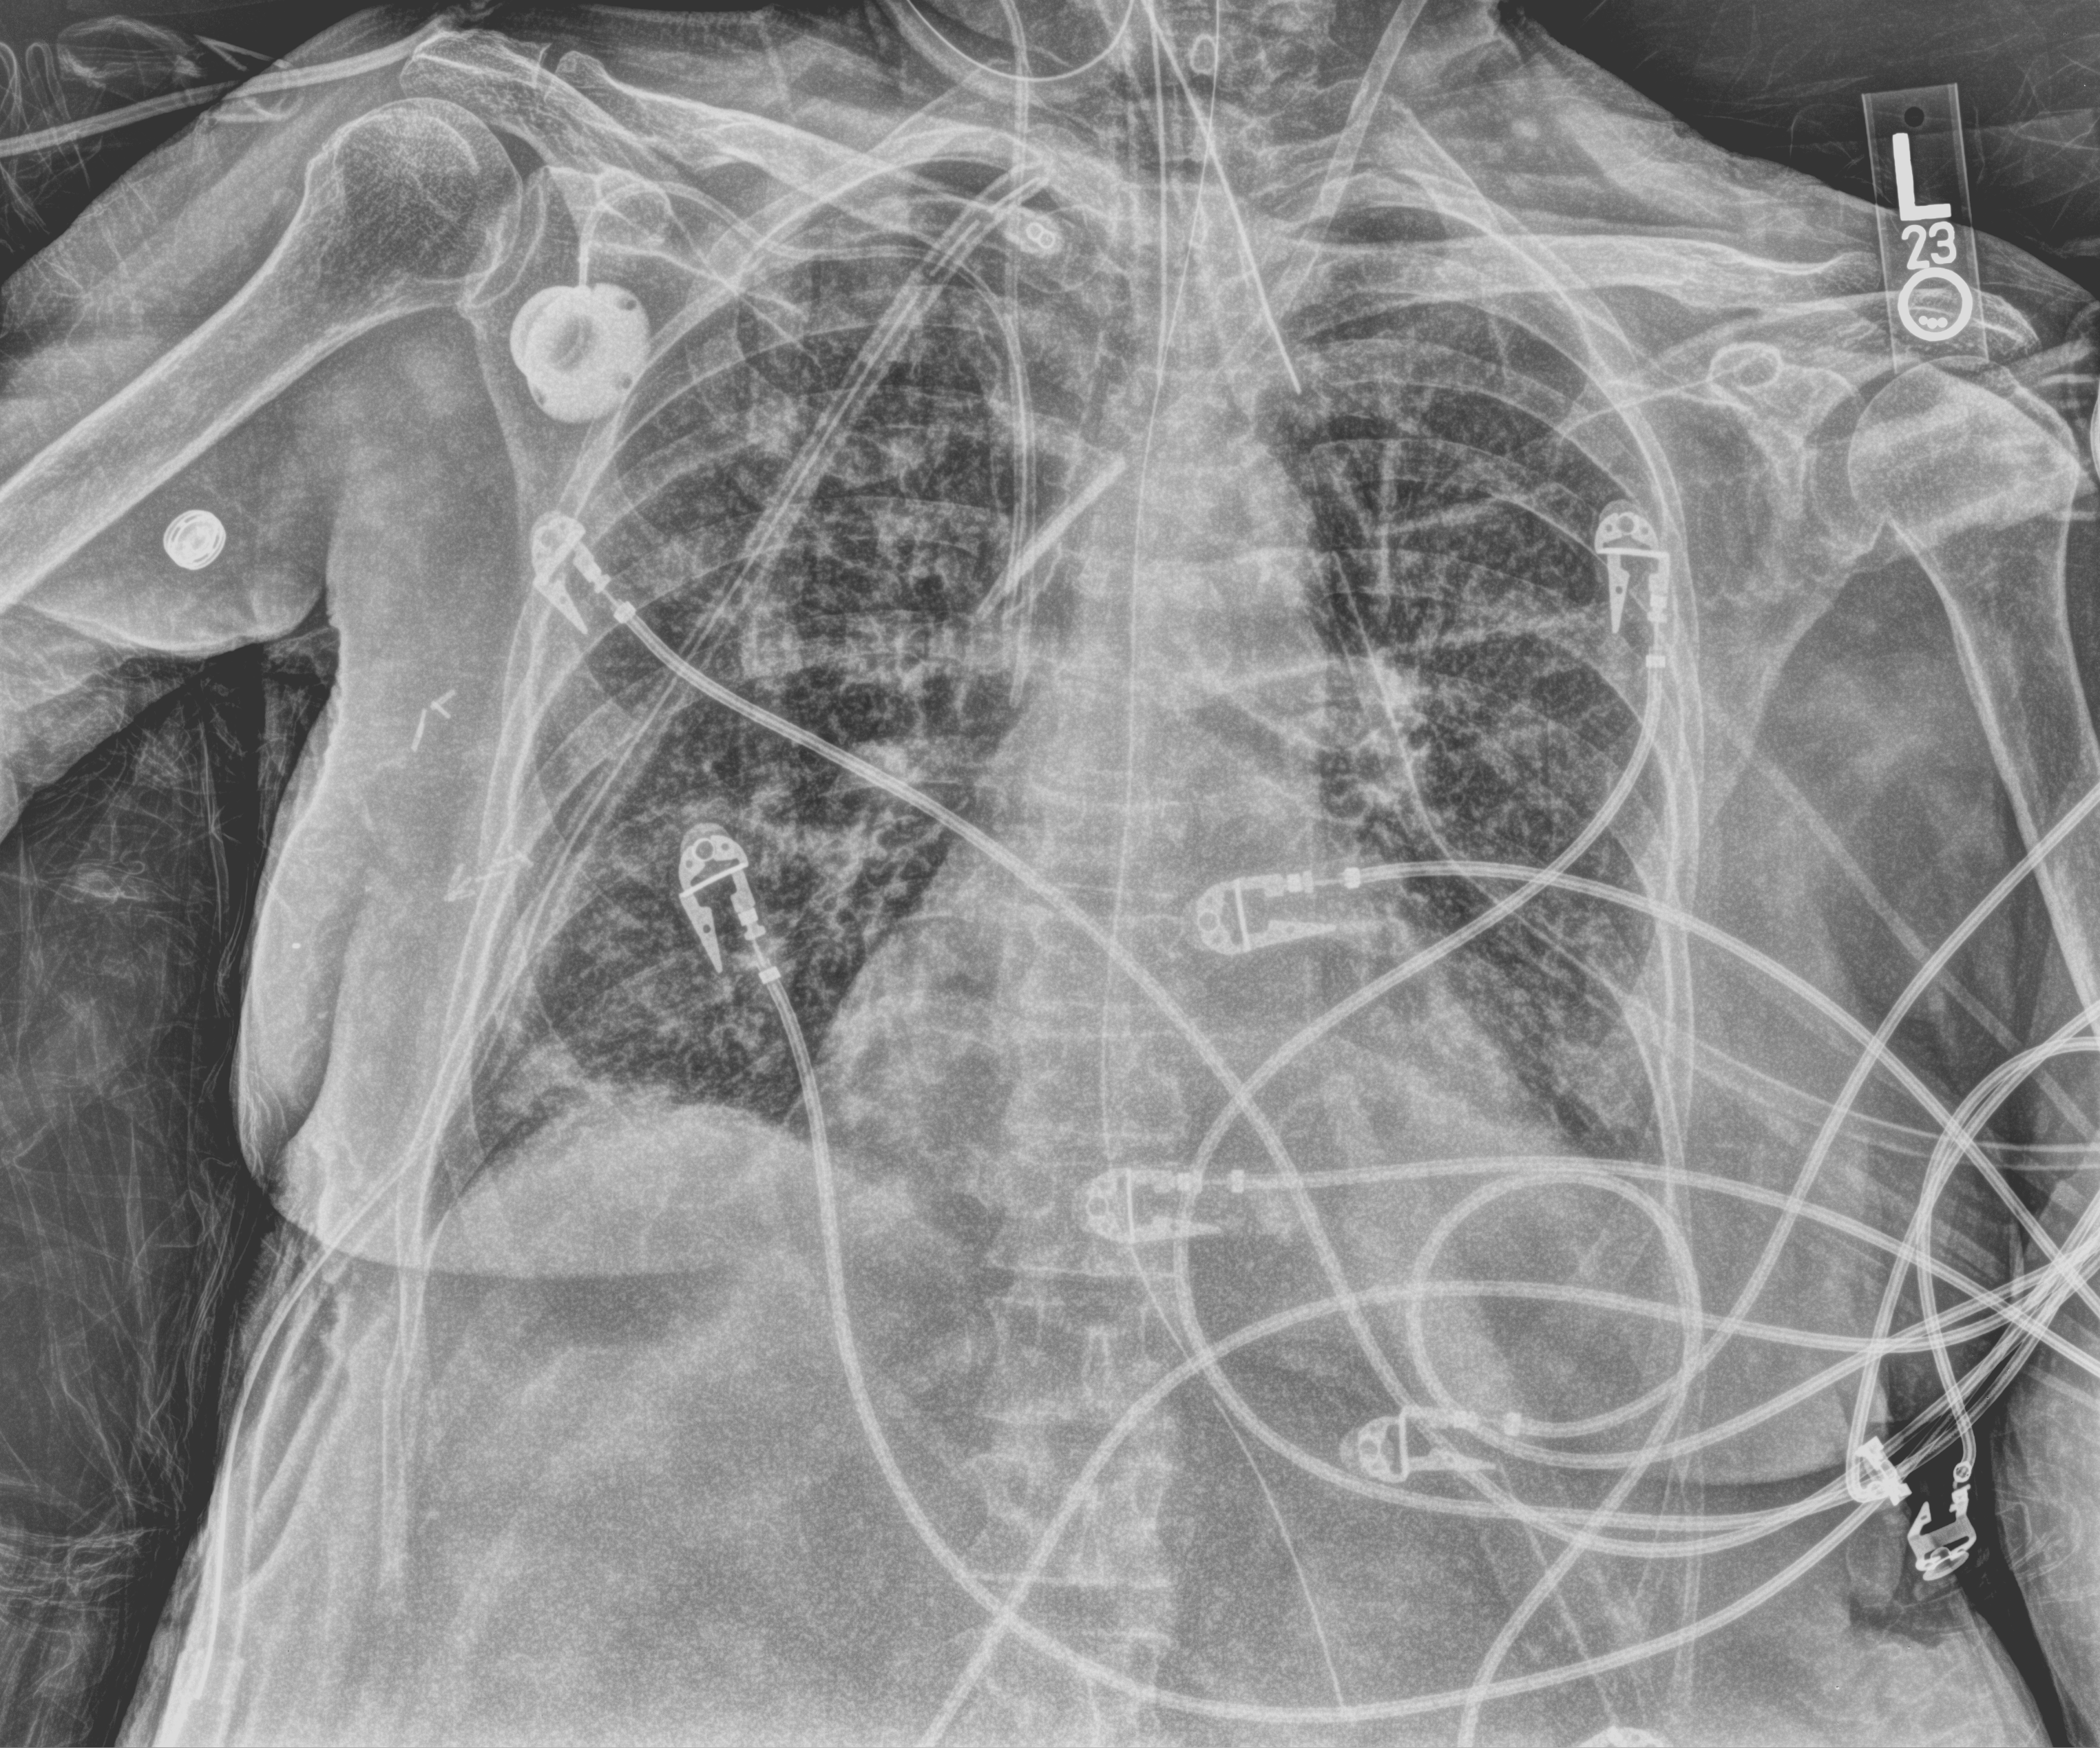
Bedside chest radiograph (computed radiography). Female patient hospitalised with COVID-19, age 60–74 years.
From the hospital-stay record, not from the radiograph (when in the stay this image was taken is not recorded):
- admitted to intensive care during this hospital stay: yes
- length of hospital stay: 43 days